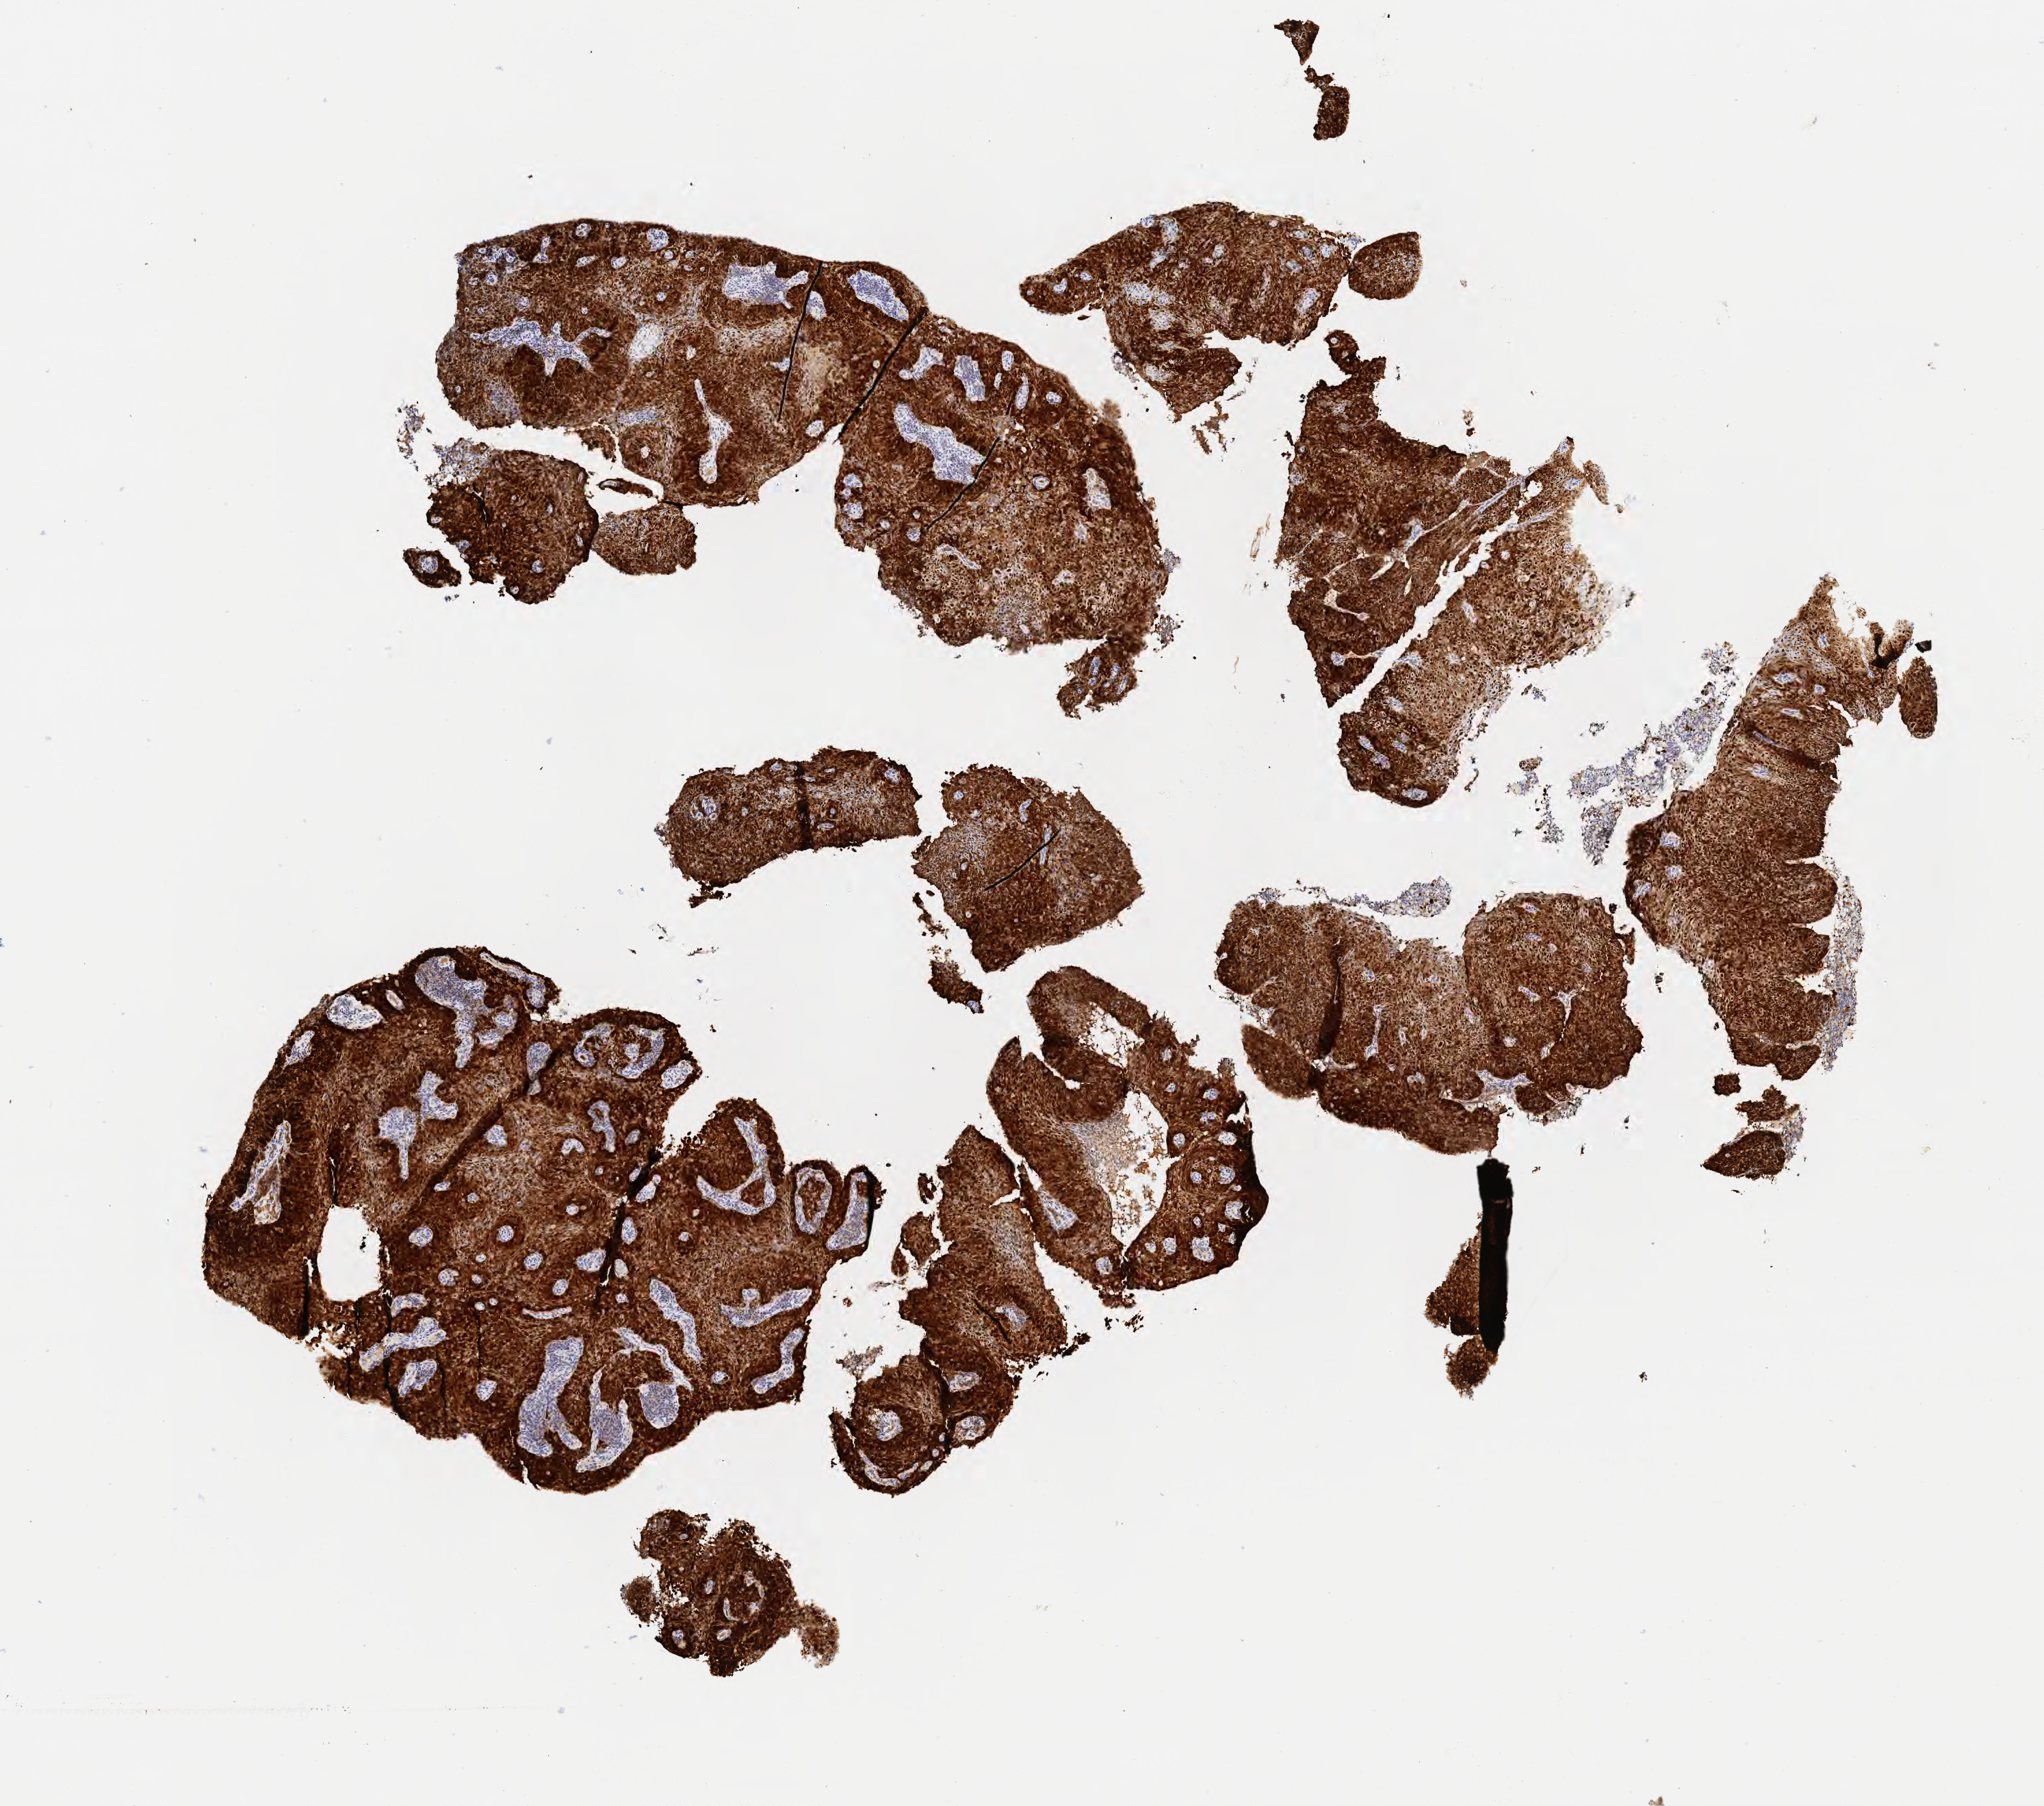
Whole-slide image, immunohistochemical stain for p16 (p16INK4a), whole scanned area (about 6.0 x 5.3 mm) shown as a low-resolution overview; tumor tissue; anatomic site: cervix. Female patient, 37 years old.
• histologic diagnosis: Squamous cell carcinoma, large cell, nonkeratinizing, NOS